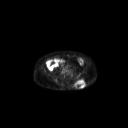
FDG PET of an extremity soft-tissue mass (from a PET/CT study), one axial slice. Slice 86 of 267 in the series (ordered by position). 128 × 128 image matrix, field of view 700 × 700 mm. Patient: male, 69 years. From the clinical record (not read from this slice): histological type: leiomyosarcoma; grade: intermediate; site of the primary tumour: left pelvis.
Annotated regions visible in this slice (expert contour drawn on MRI and transferred to this co-registered scan by the dataset authors):
- gross tumour volume (mass): bounding box (x1, y1, x2, y2) in pixels: (74, 79, 86, 89)